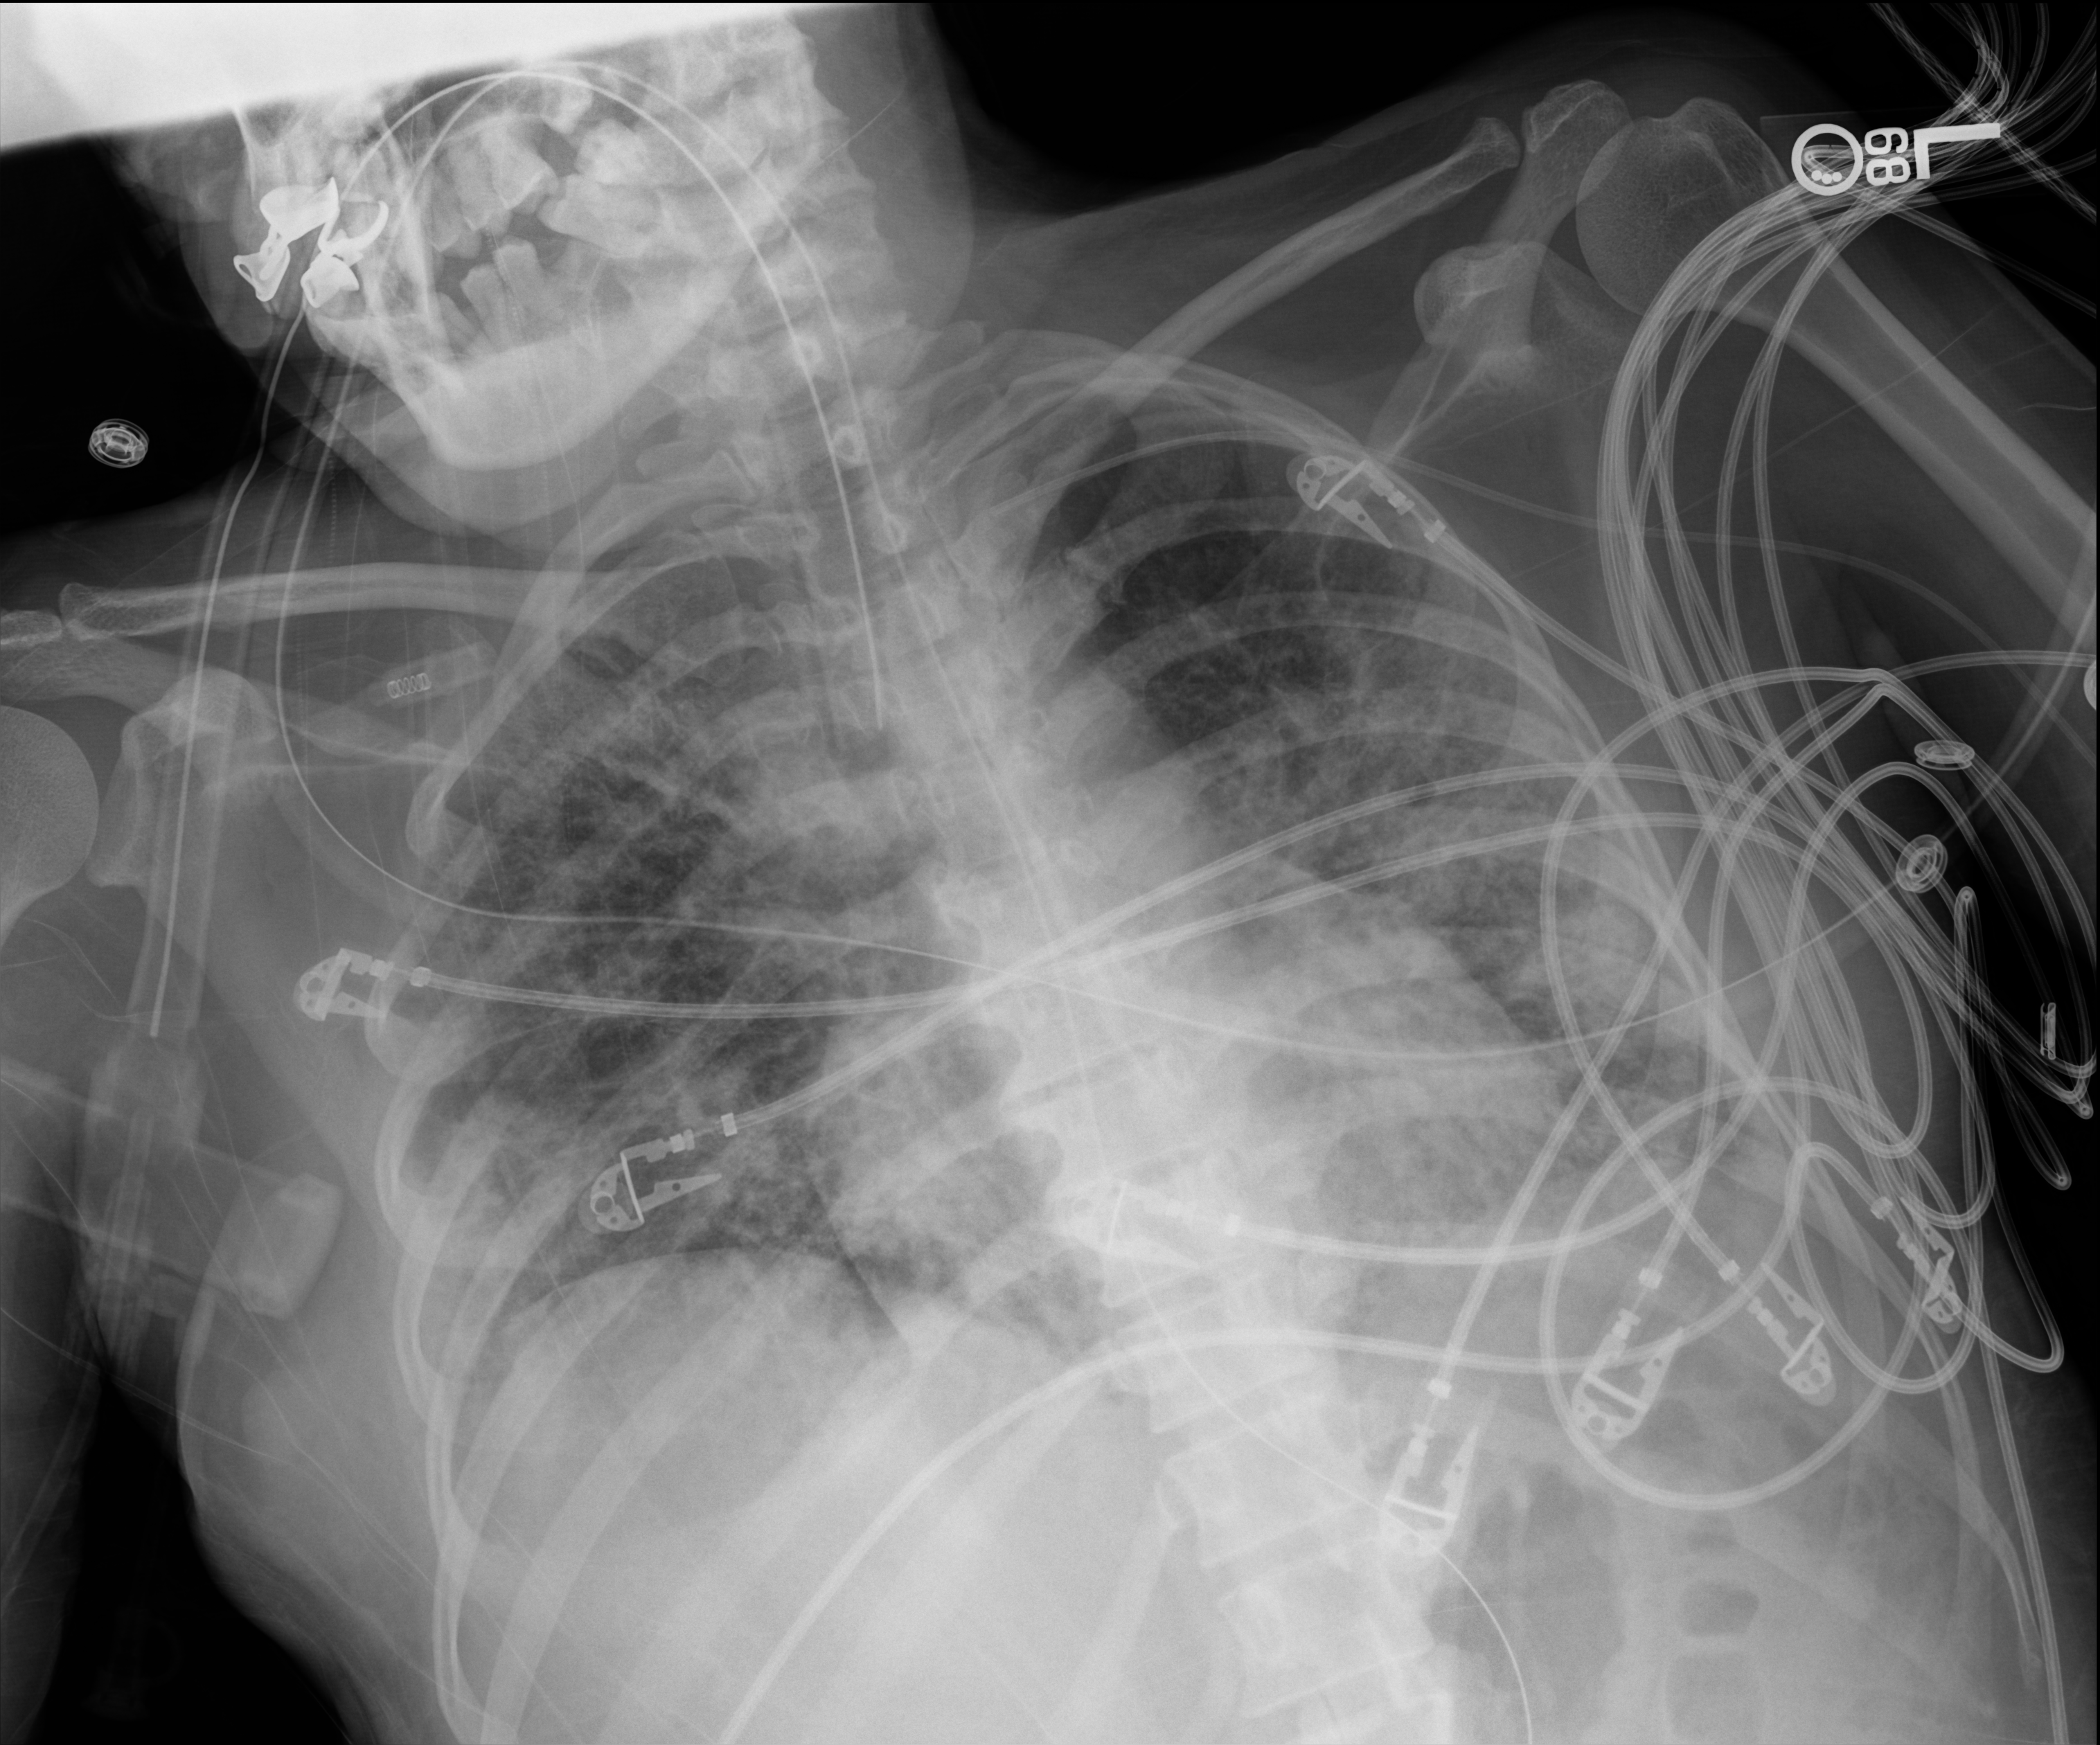
Bedside chest radiograph (digital radiography); anteroposterior (AP) projection. Patient hospitalised with COVID-19; female, aged 18–59 years.
Hospital-stay facts (about this admission, not read from this image; timing relative to this image not recorded): mechanically ventilated during this hospital stay: yes; COPD (admission record): no.